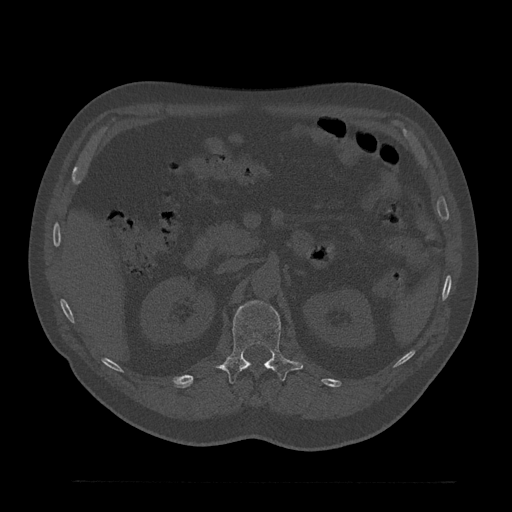
CT including the spine, one axial slice; slice 175 of 797 in the series (ordered by position); bone window (W 1800 / L 400 HU); 0.5 mm slice thickness; 512 × 512 image matrix. Patient: male, 61 years. Case-level facts recorded for this patient, not image findings: primary cancer: prostate.
Structures marked on this image (semi-automatic segmentation, software-assisted and operator-edited):
- L1 vertebra: bounding box (x1, y1, x2, y2) in pixels: (220, 300, 303, 384)